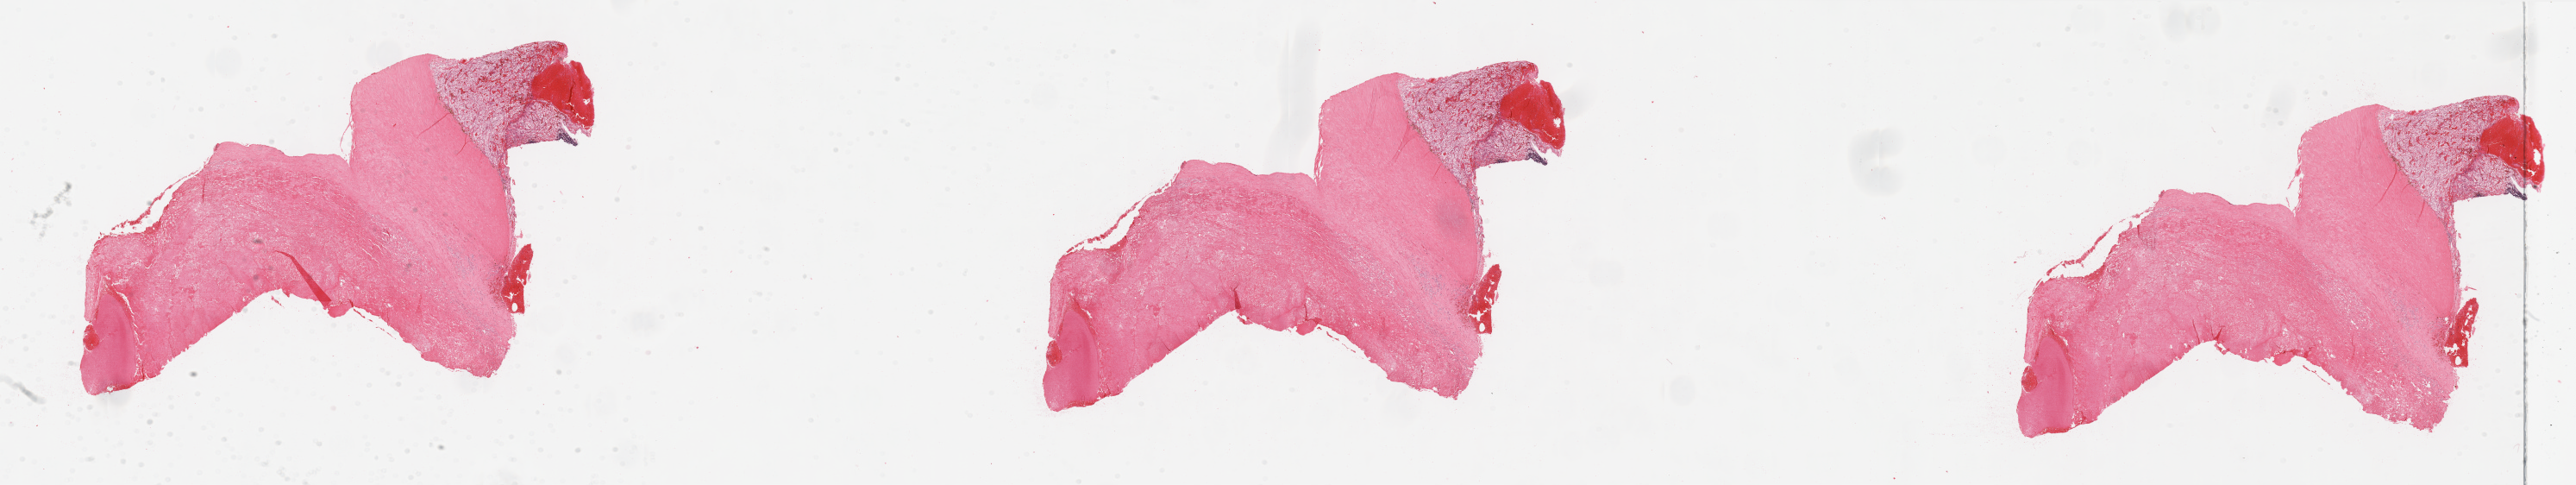
H&E whole-slide image, a low-resolution overview of the entire scanned area, about 47.3 x 8.9 mm (from a 20x scan), tumour tissue sample, sampled site: kidney. Female, 51 y/o. Histologic grade: G3 (poorly differentiated). Composition of this section per pathologist review: tumour nuclei 80%, necrosis 70%.
* AJCC pathologic stage: IV
* diagnosis: Renal cell carcinoma, NOS